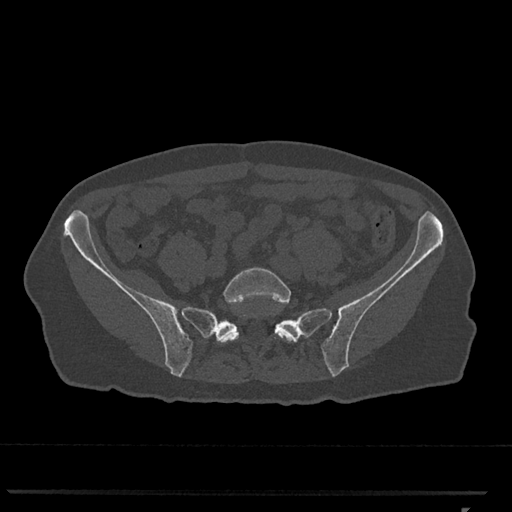
CT including the spine, one axial slice; slice 124 of 793 in the series (ordered by position); 120 kVp; bone window (W 1800 / L 400 HU); 0.5 mm slice thickness; 512 × 512 image matrix. Patient: female, 62 years. From the clinical record (not read from this slice): primary cancer: renal.
Structures marked on this image (semi-automatic segmentation, software-assisted and operator-edited):
- L5 vertebra: bounding box <219,267,297,343> (left, top, right, bottom; pixels)